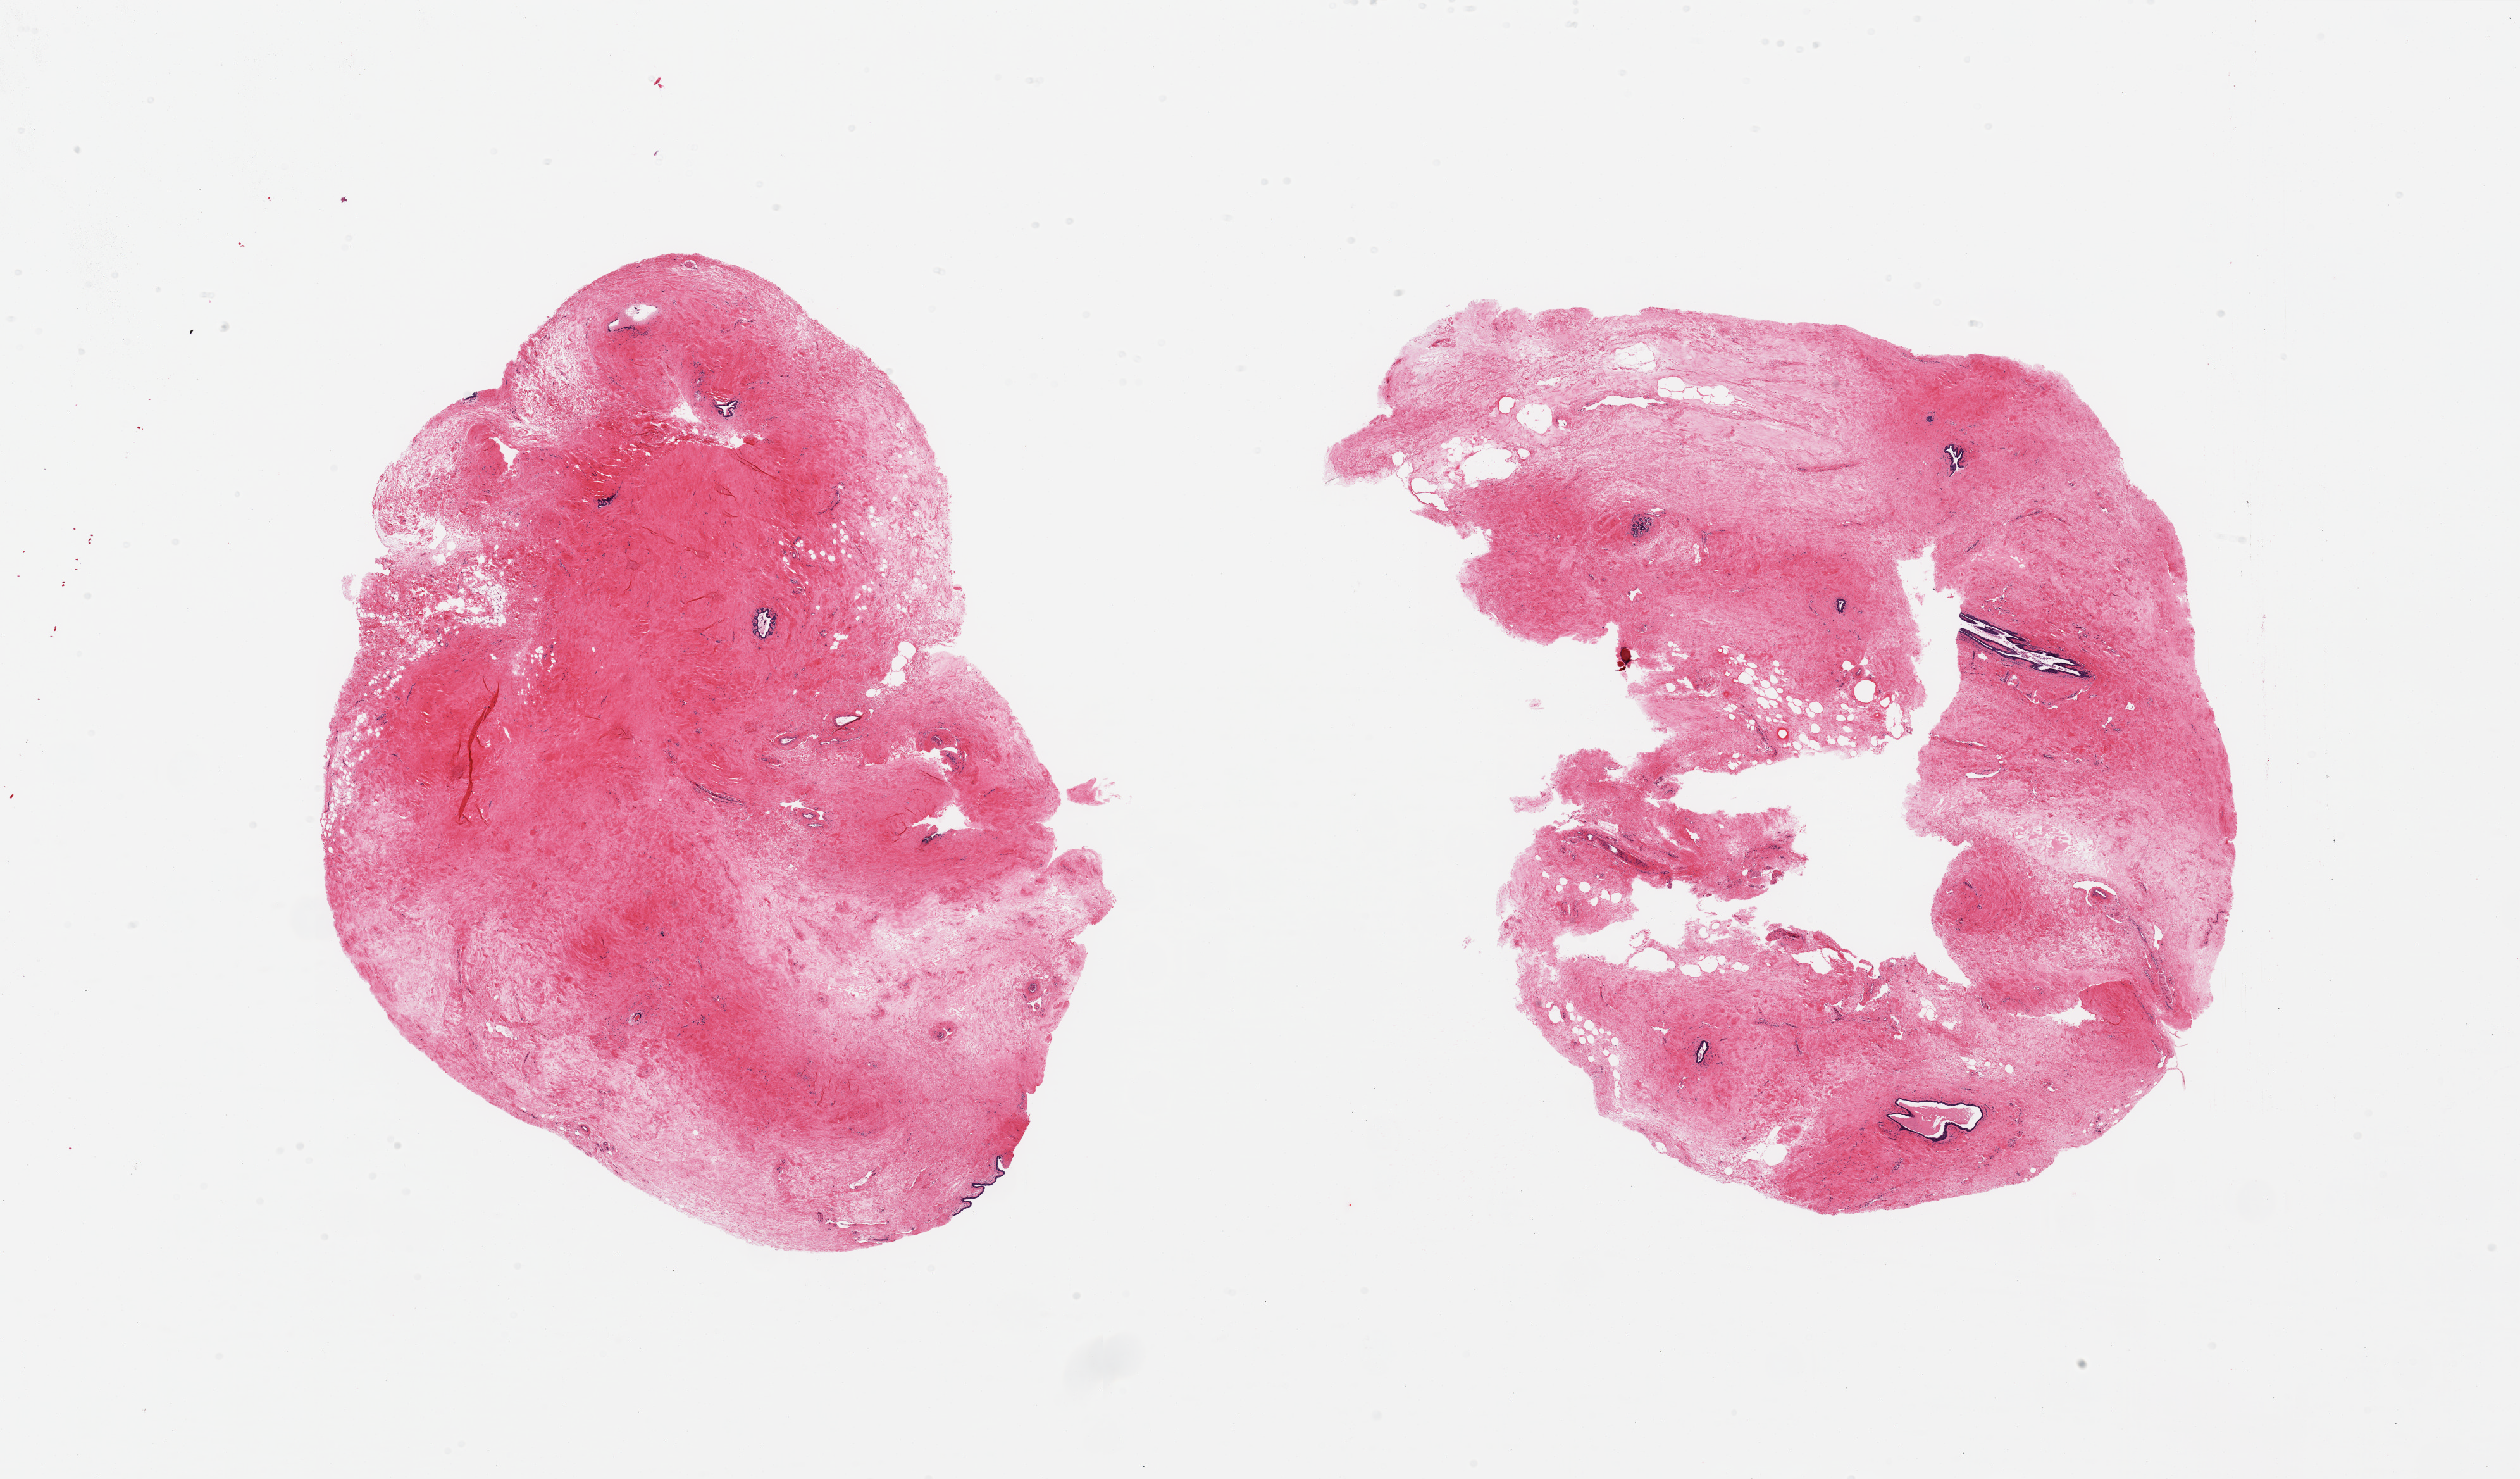
Digitized hematoxylin and eosin (H&E)-stained section — shown as a low-resolution overview of the whole scanned area (about 31.5 x 18.5 mm, acquisition: 20x scan). PAXgene-fixed, paraffin-embedded tissue. Target tissue: breast. Donor tissue sample. Donor: female.
Reviewer comment on this tissue sample: 2 pieces; fibrocollagenous stroma with scattered ducts/TDLUs.